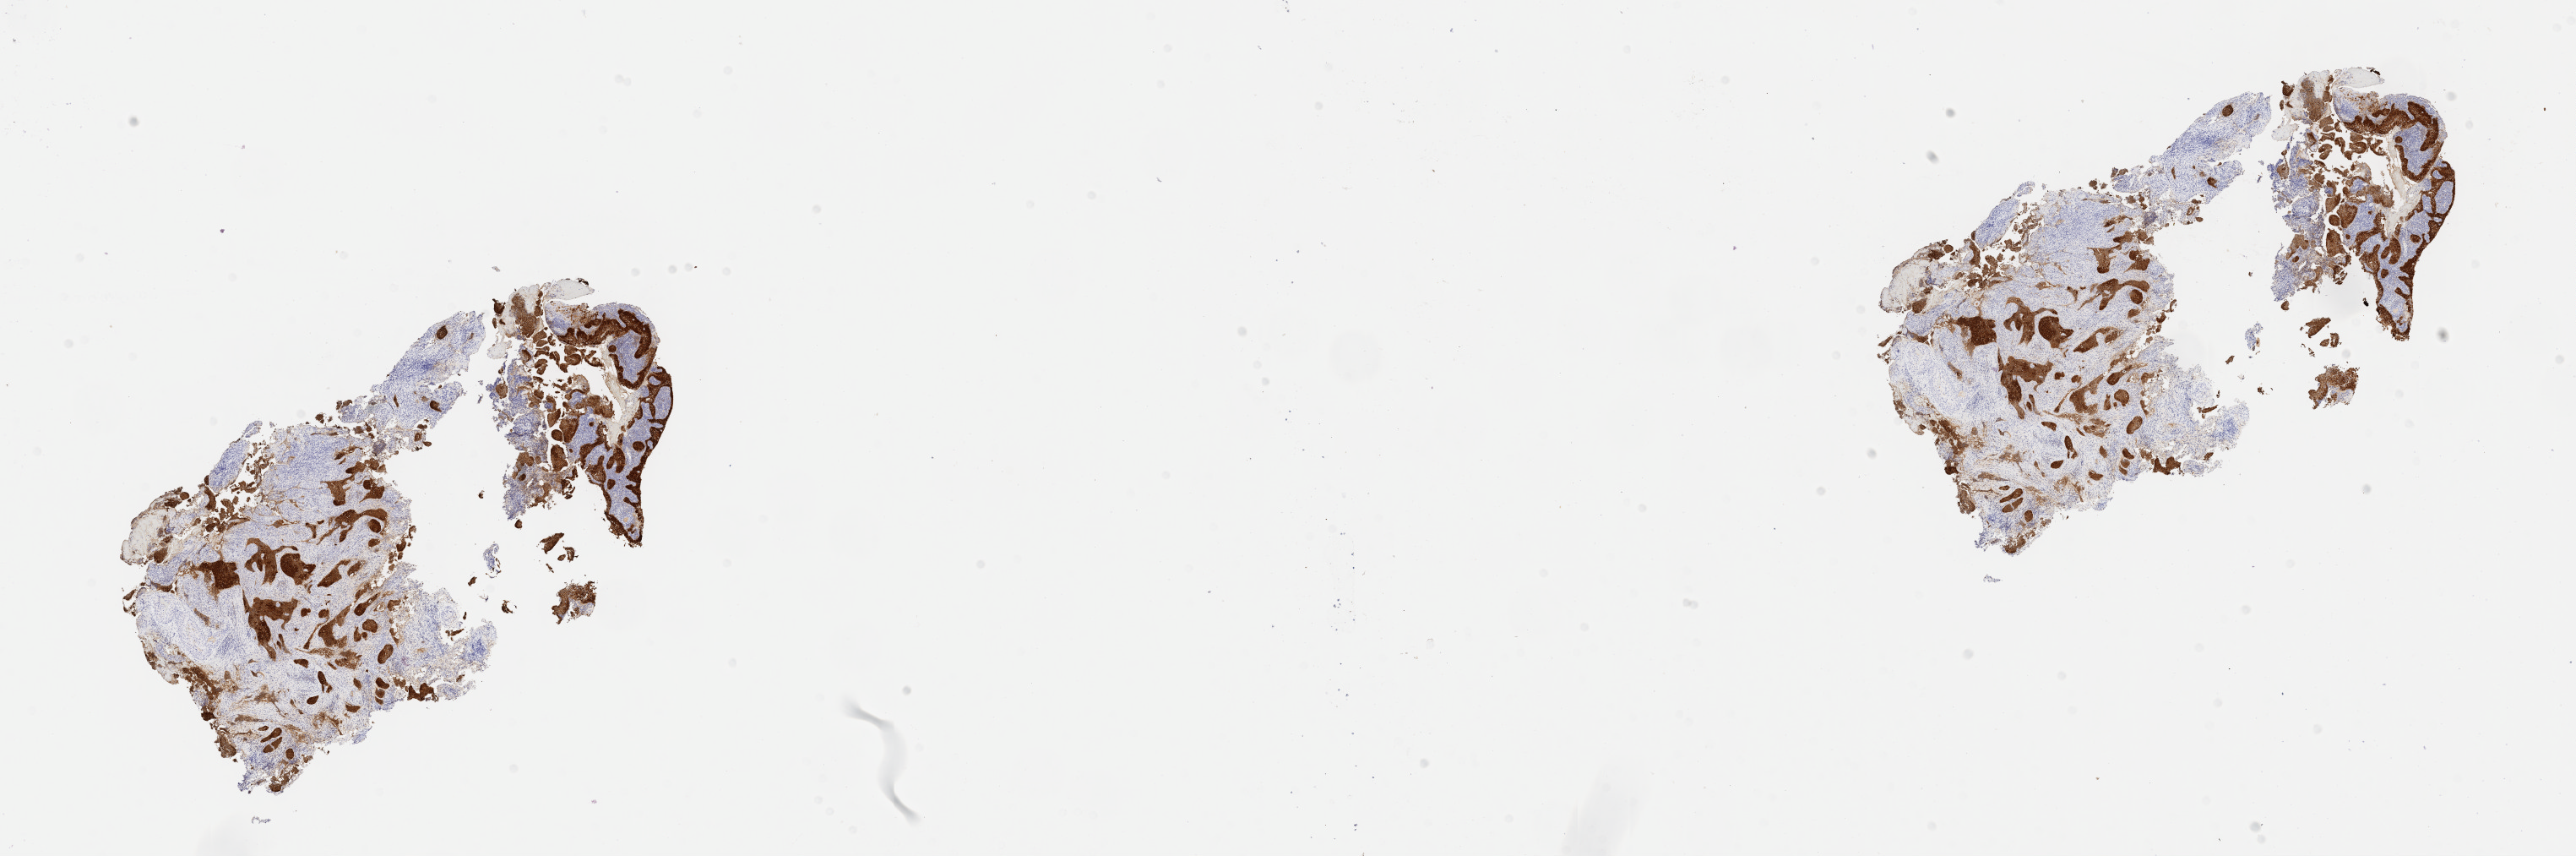
Whole-slide image, immunohistochemical stain for p16 (p16INK4a) — low-resolution overview of the scanned area, about 24.7 x 8.2 mm; specimen: tumor tissue; anatomic site: cervix. Female patient, age 28 years.
Diagnosis: Squamous cell carcinoma, large cell, nonkeratinizing, NOS.